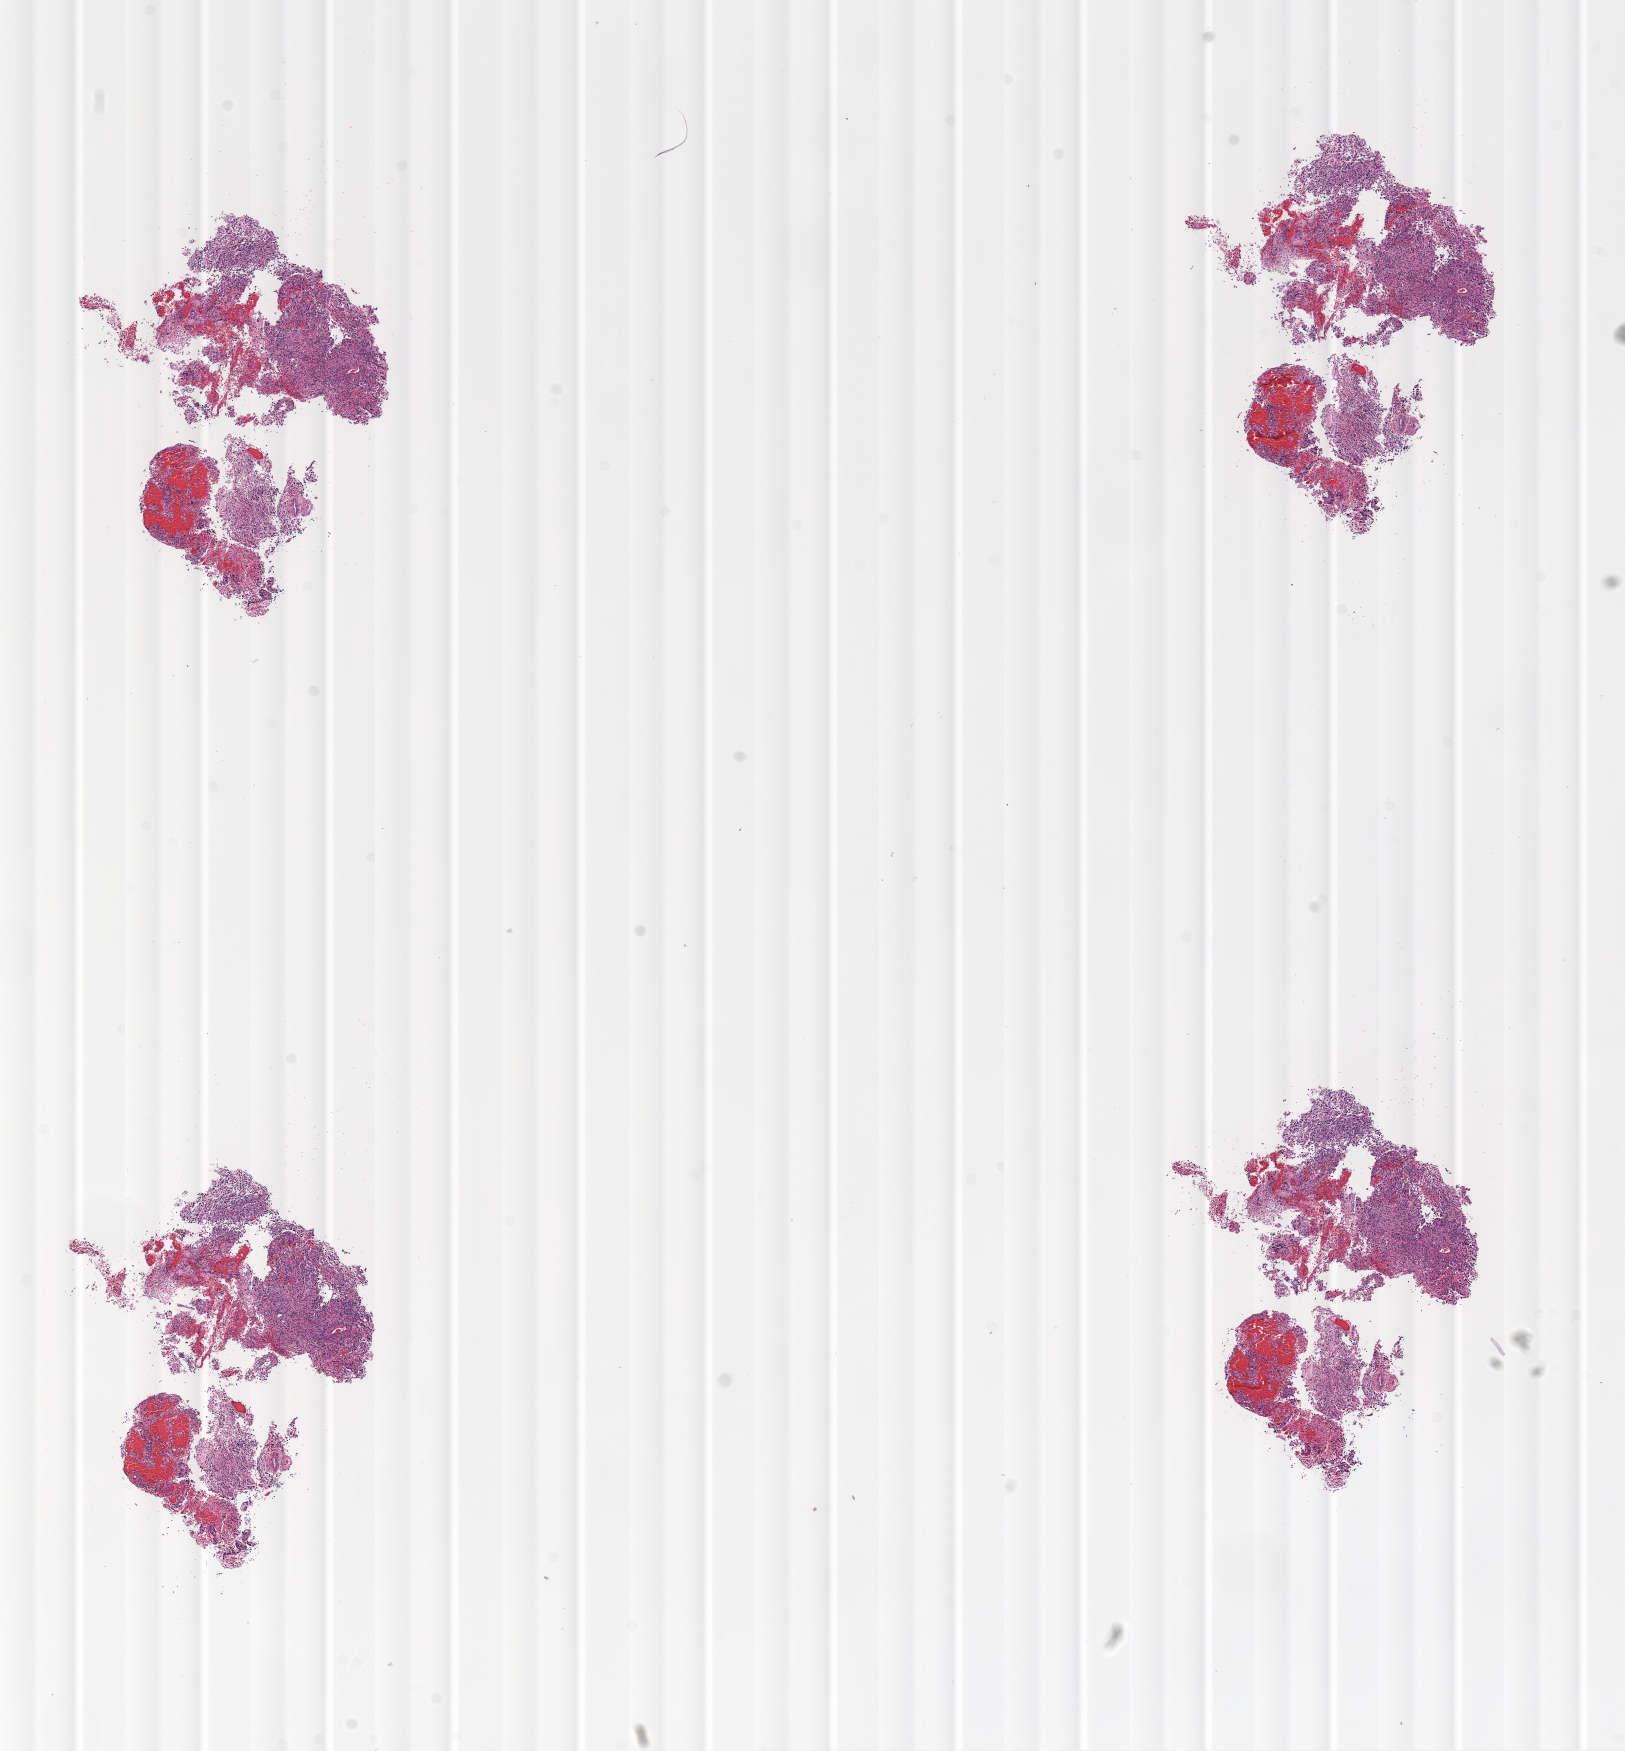
Whole-slide histology image, Hematoxylin and eosin (H&E) stained, shown as a low-resolution overview of the whole scanned area (about 13.0 x 14.1 mm). Formalin-fixed paraffin-embedded (FFPE) diagnostic section. Primary tumour sample from the brain. Female, age 61 years at initial diagnosis.
• diagnosis: Glioblastoma